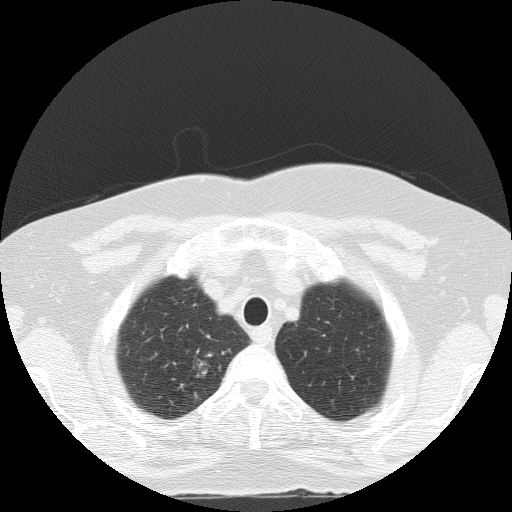
Low-dose screening chest CT, one axial slice; position 117 of 133 along the scan axis; reconstruction kernel FC51; 120 kVp; lung window (W 1500 / L -600 HU); 2 mm slice thickness; 512 × 512 image matrix.
Outlined on this slice (manually delineated by an expert):
- lesion 1 (tumor, upper lobe of right lung): bounding box [x1, y1, x2, y2] px = [198, 354, 213, 376]